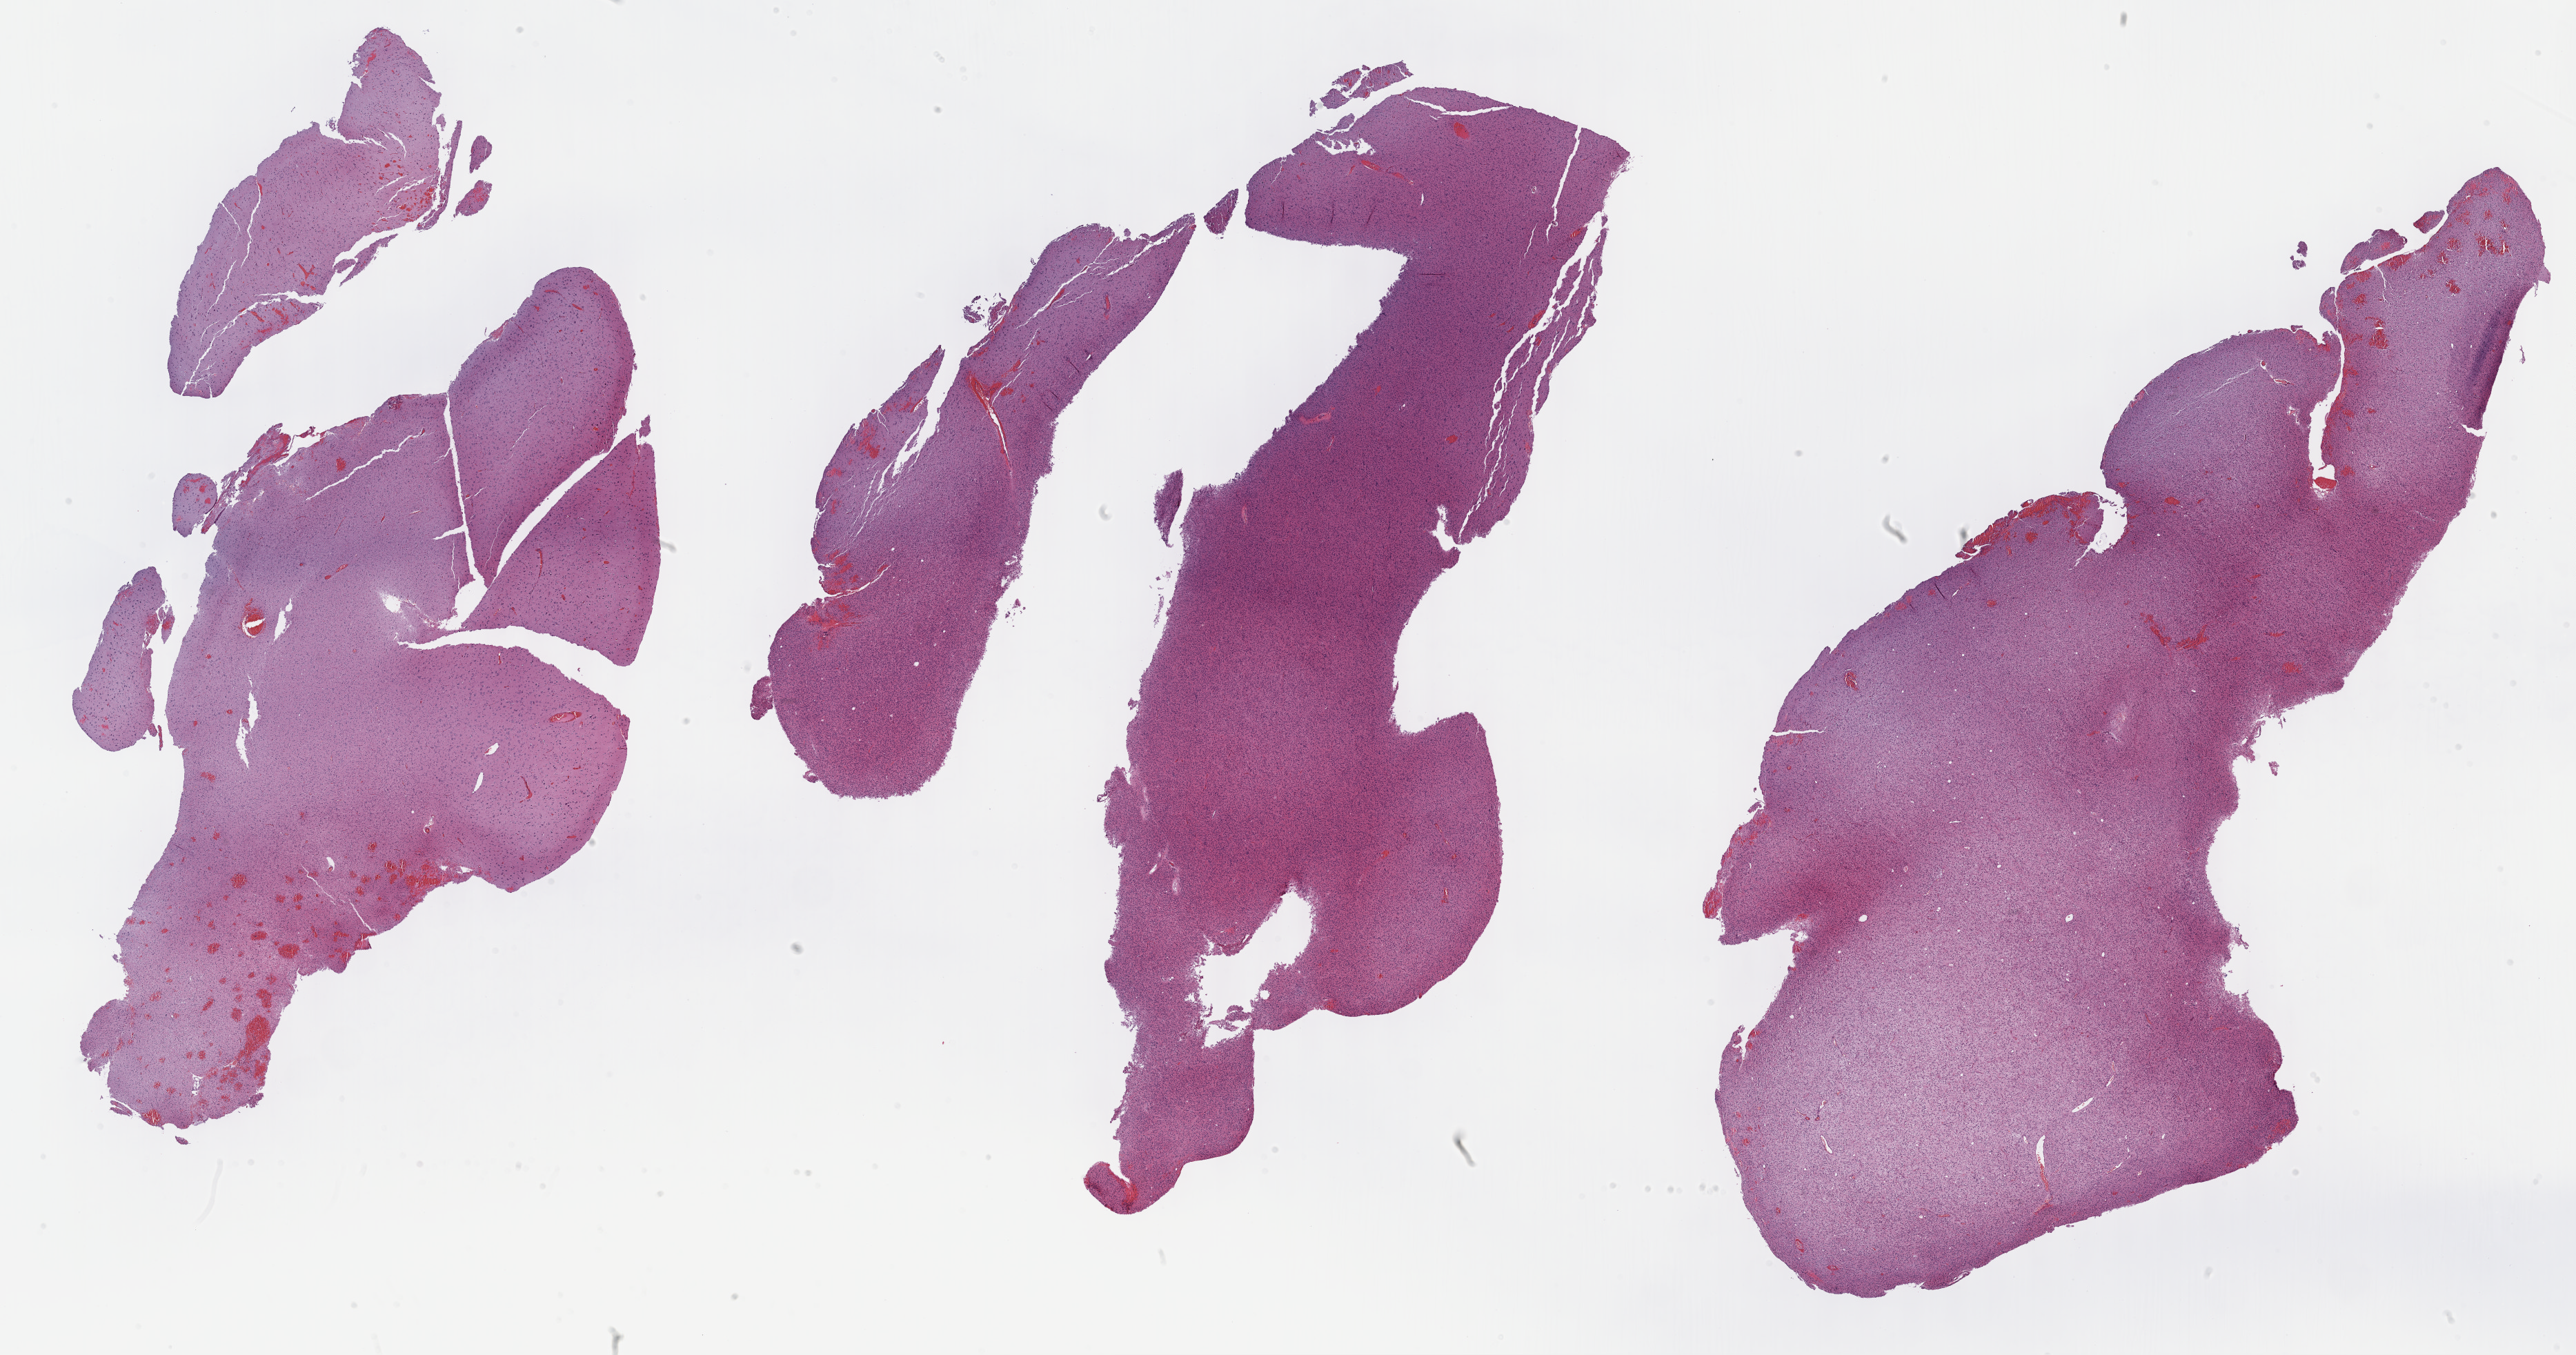
Digitized H&E-stained tissue section (whole slide), whole scanned area (about 30.2 x 15.9 mm, acquisition: 40x scan) shown as a low-resolution overview, formalin-fixed paraffin-embedded (FFPE) diagnostic section, primary tumour sample from the brain. Male, age 25 years at initial diagnosis. Histologic grade: G2 (moderately differentiated).
• histologic diagnosis: Oligodendroglioma, NOS (cerebrum)
• laterality: left